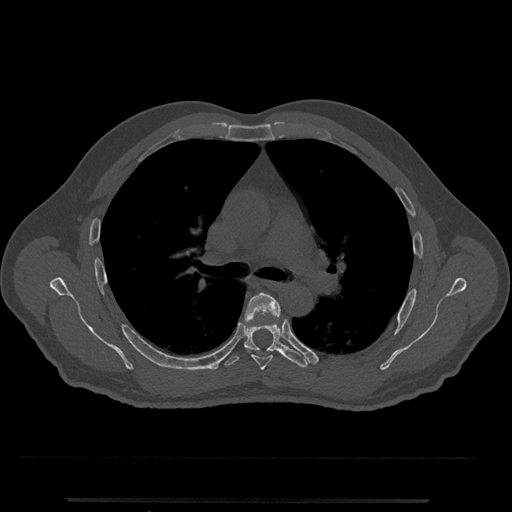
CT including the spine, one axial slice; slice 765 of 797 in the series (ordered by position); reconstruction kernel Br40s/3; 120 kVp; bone window (W 1800 / L 400 HU); 0.5 mm slice thickness; 512 × 512 image matrix, field of view 419 × 419 mm. Patient: male, 63 years. From the clinical record (not read from this slice): primary cancer: prostate.
Structures marked on this image (semi-automatic segmentation, software-assisted and operator-edited):
- T5 vertebra: bounding box (x1, y1, x2, y2) in pixels: (244, 292, 281, 370)
- T6 vertebra: (224, 319, 309, 368)